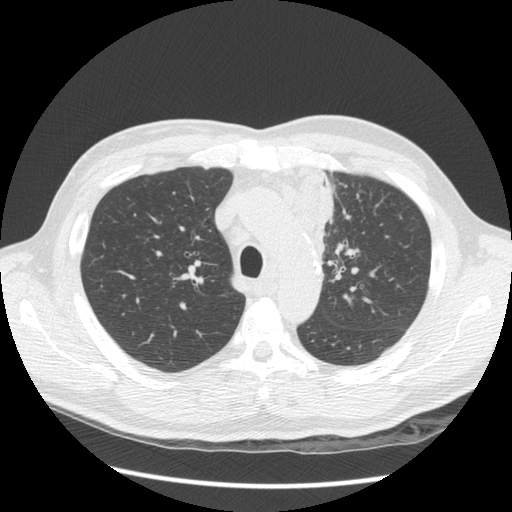
Low-dose screening chest CT, one axial slice. Position 102 of 136 along the scan axis. 120 kVp. Lung window (W 1500 / L -600 HU). 2.5 mm slice thickness. 512 × 512 image matrix, field of view 360 × 360 mm.
Annotated regions visible in this slice (expert manual segmentation):
- lesion 1 (tumor, upper lobe of left lung): bounding box (x1, y1, x2, y2) in pixels: (299, 172, 333, 255)